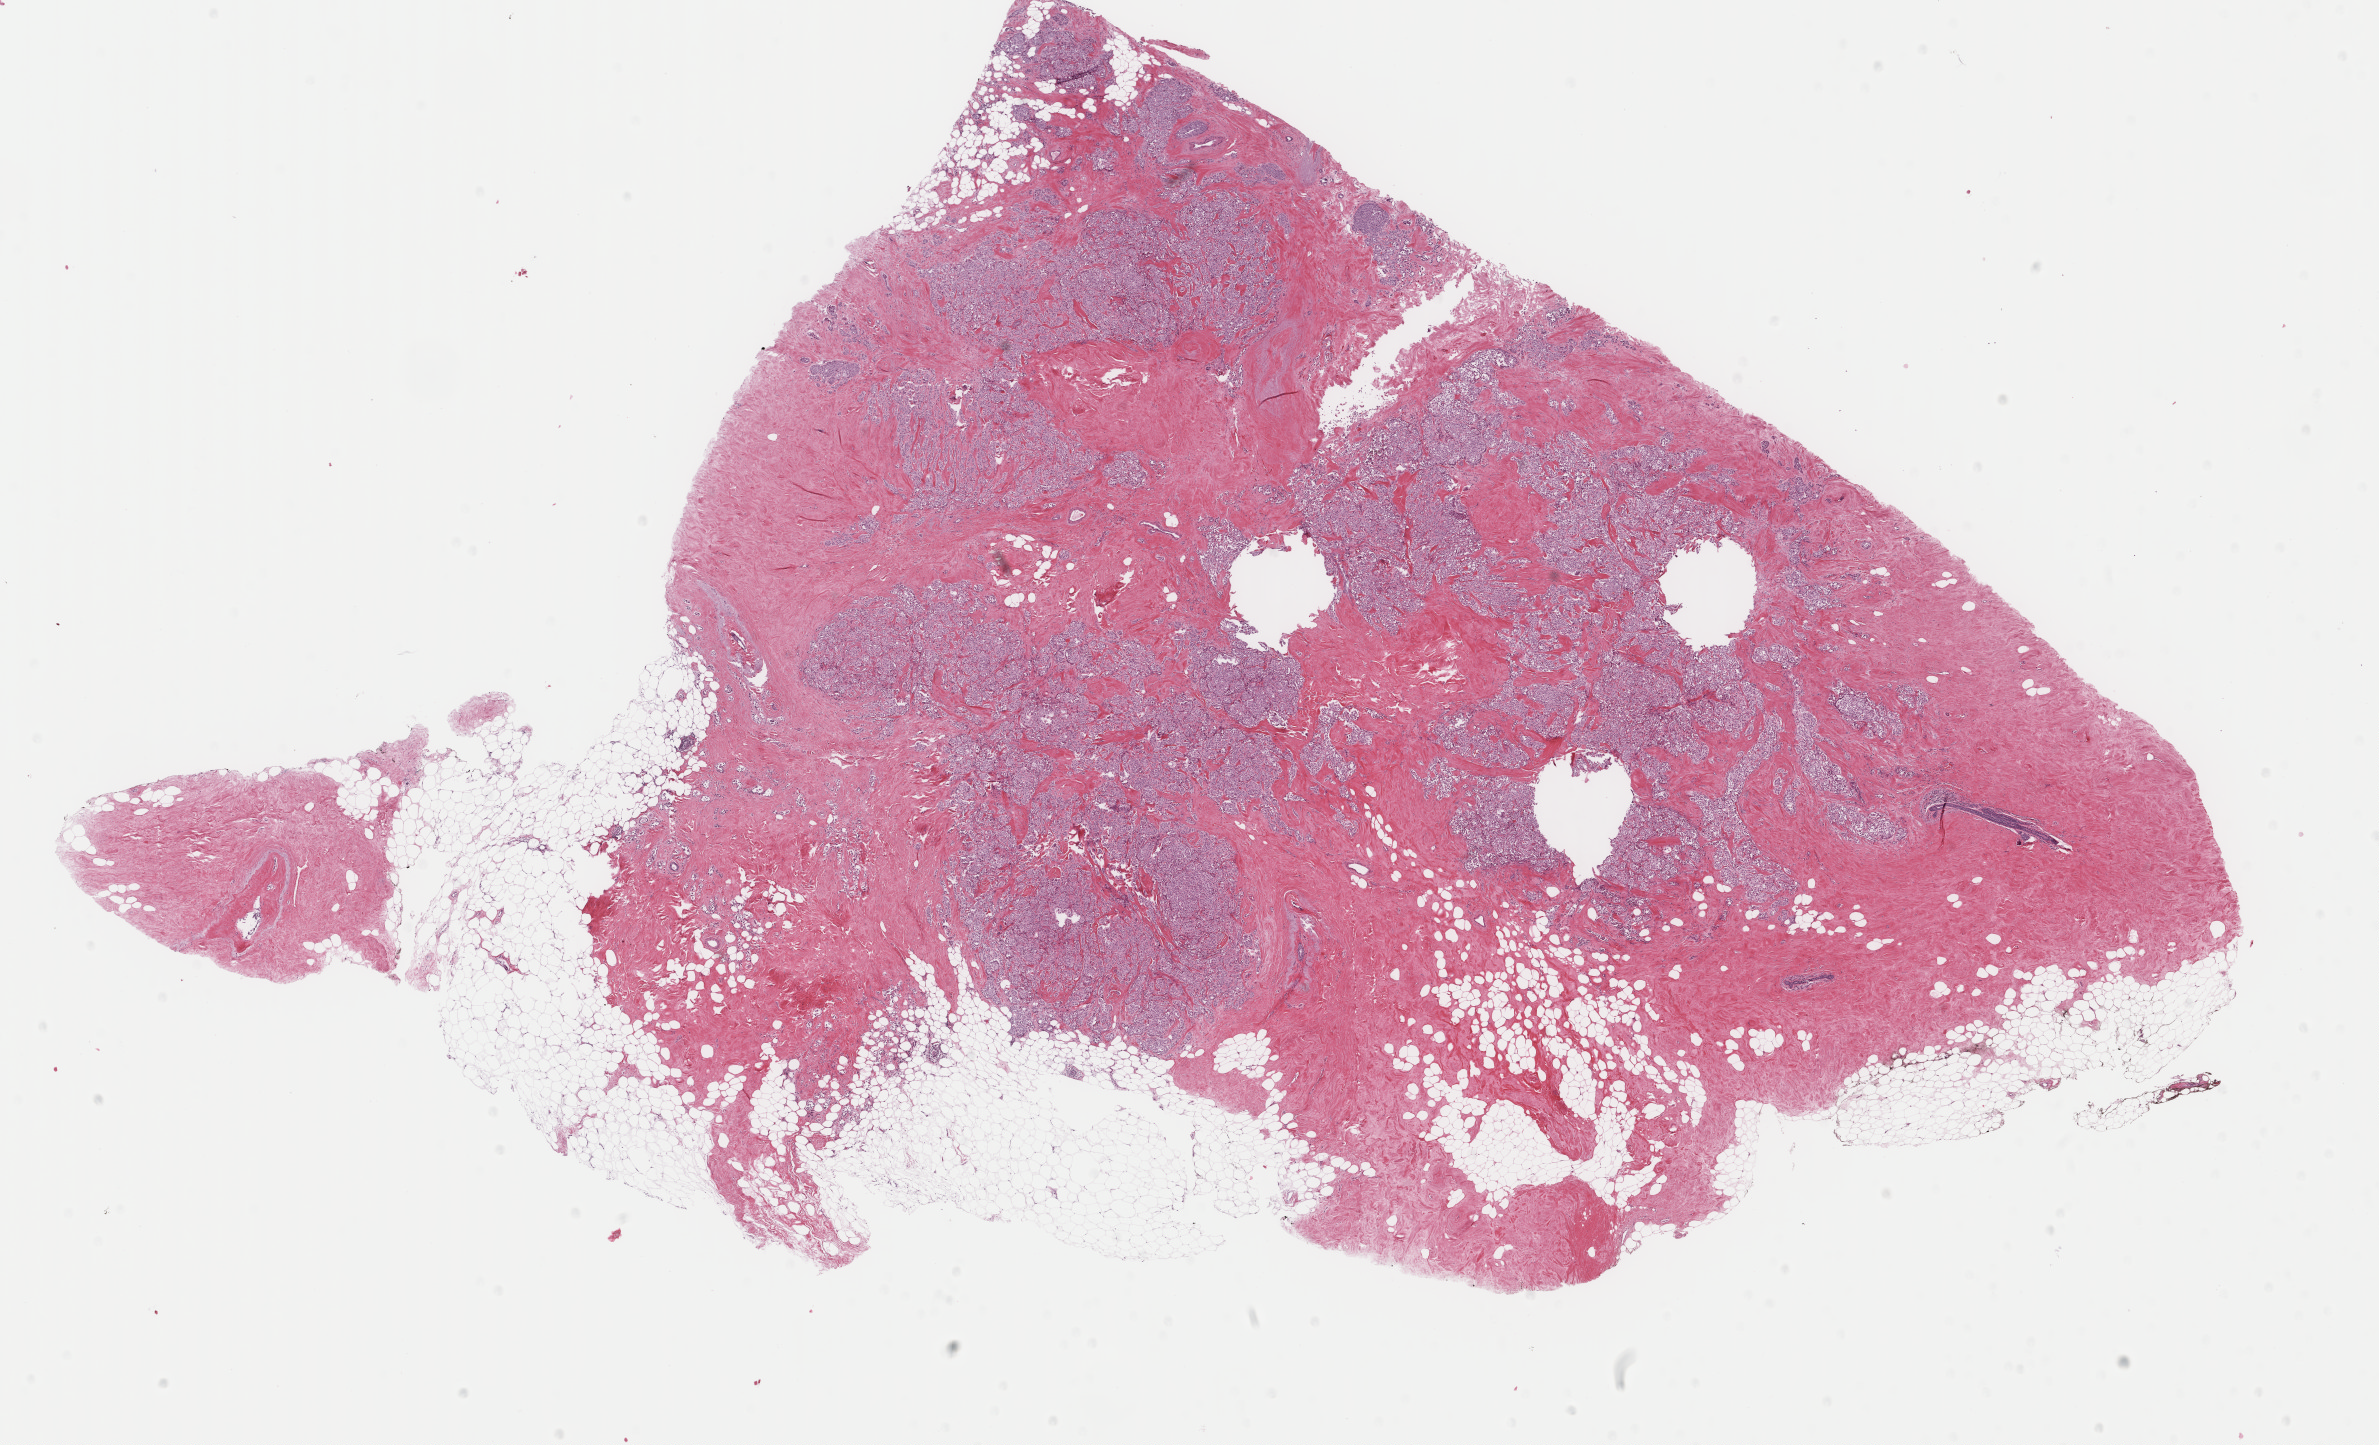
Digitized H&E tissue section (whole slide) — whole scanned area (about 18.9 x 11.5 mm, slide scanned at 40x) shown as a low-resolution overview. Formalin-fixed paraffin-embedded (FFPE) diagnostic section. Primary tumour sample from the breast. Female, age 69 years at initial diagnosis.
Histologic diagnosis: Lobular carcinoma, NOS.